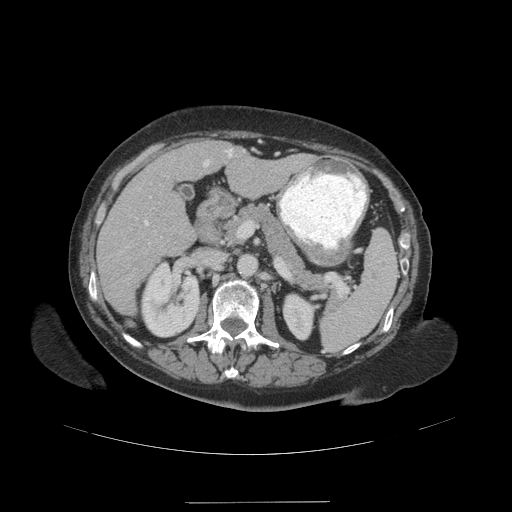
Contrast-enhanced abdominal CT (liver protocol), one axial slice. Slice 55 of 99 in the series (ordered by position). Soft-tissue window (W 400 / L 40 HU). 2.5 mm slice thickness. 512 × 512 image matrix, field of view 440 × 440 mm. From the clinical record (not read from this slice): diagnosis: hepatocellular carcinoma (patient treated with transarterial chemoembolisation; whether this scan precedes or follows treatment is not stated here); TNM stage (as recorded): Stage-IVA; Child-Pugh class: A.
Outlined on this slice (semi-automatically segmented with operator editing):
- liver parenchyma outside the tumour (the mass and vessels are separate outlines, so this box may not span the whole liver): bounding box [x1, y1, x2, y2] px = [96, 138, 311, 314]
- liver vessels: [145, 149, 233, 226]